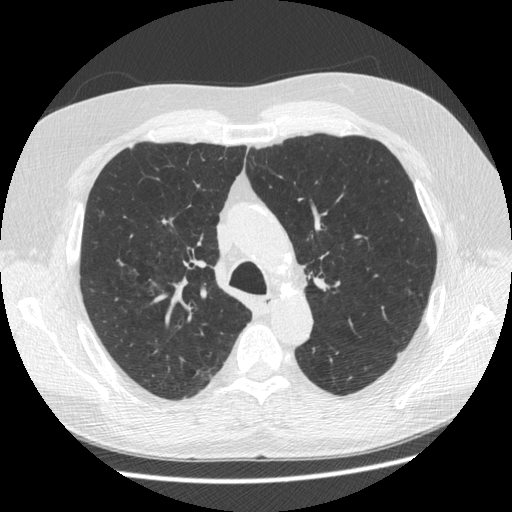
Chest CT (low-dose screening protocol), one axial image, third annual screen, lung window (W 1500 / L -600 HU), 1.25 mm slice thickness, standard (soft-tissue) reconstruction kernel (STANDARD), 512 × 512 image matrix, field of view 360 × 360 mm. Male, age 63 years at enrolment. Former smoker at enrolment.
Lesion marked by an expert reader, box from (x=150, y=207) to (x=184, y=238) px. The screening reader recorded 2 non-calcified nodules or masses ≥4 mm on this exam; which of them this box marks is not recorded. Participant outcome: lung cancer diagnosed 342 days after this screen — adenocarcinoma, NOS, right upper lobe, stage IIA (AJCC 6th edition), 8 mm at pathology.